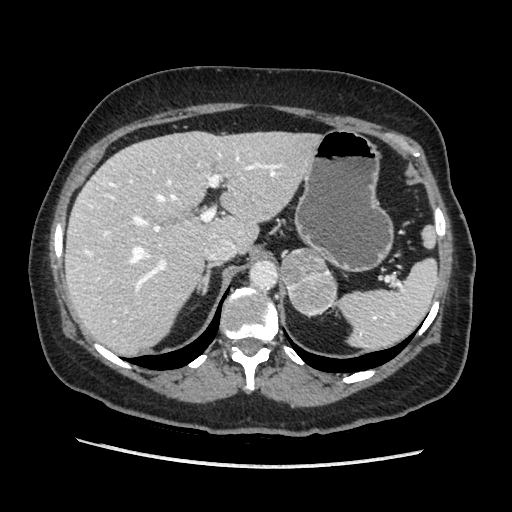
Contrast-enhanced abdominal CT, one axial slice; position 137 of 203 along the scan axis; soft-tissue window (W 400 / L 40 HU); 1.25 mm slice thickness; 512 × 512 image matrix, field of view 360 × 360 mm. Female patient. Case-level facts recorded for this patient, not image findings: diagnosis: adrenocortical carcinoma; tumour side: left adrenal; tumour size at pathology: 6.5 cm; Ki-67 index: 22 %; stage (as recorded): 2.
Structures marked on this image (semi-automatically segmented with operator editing):
- mass: bounding box [x1, y1, x2, y2] px = [281, 248, 336, 313]